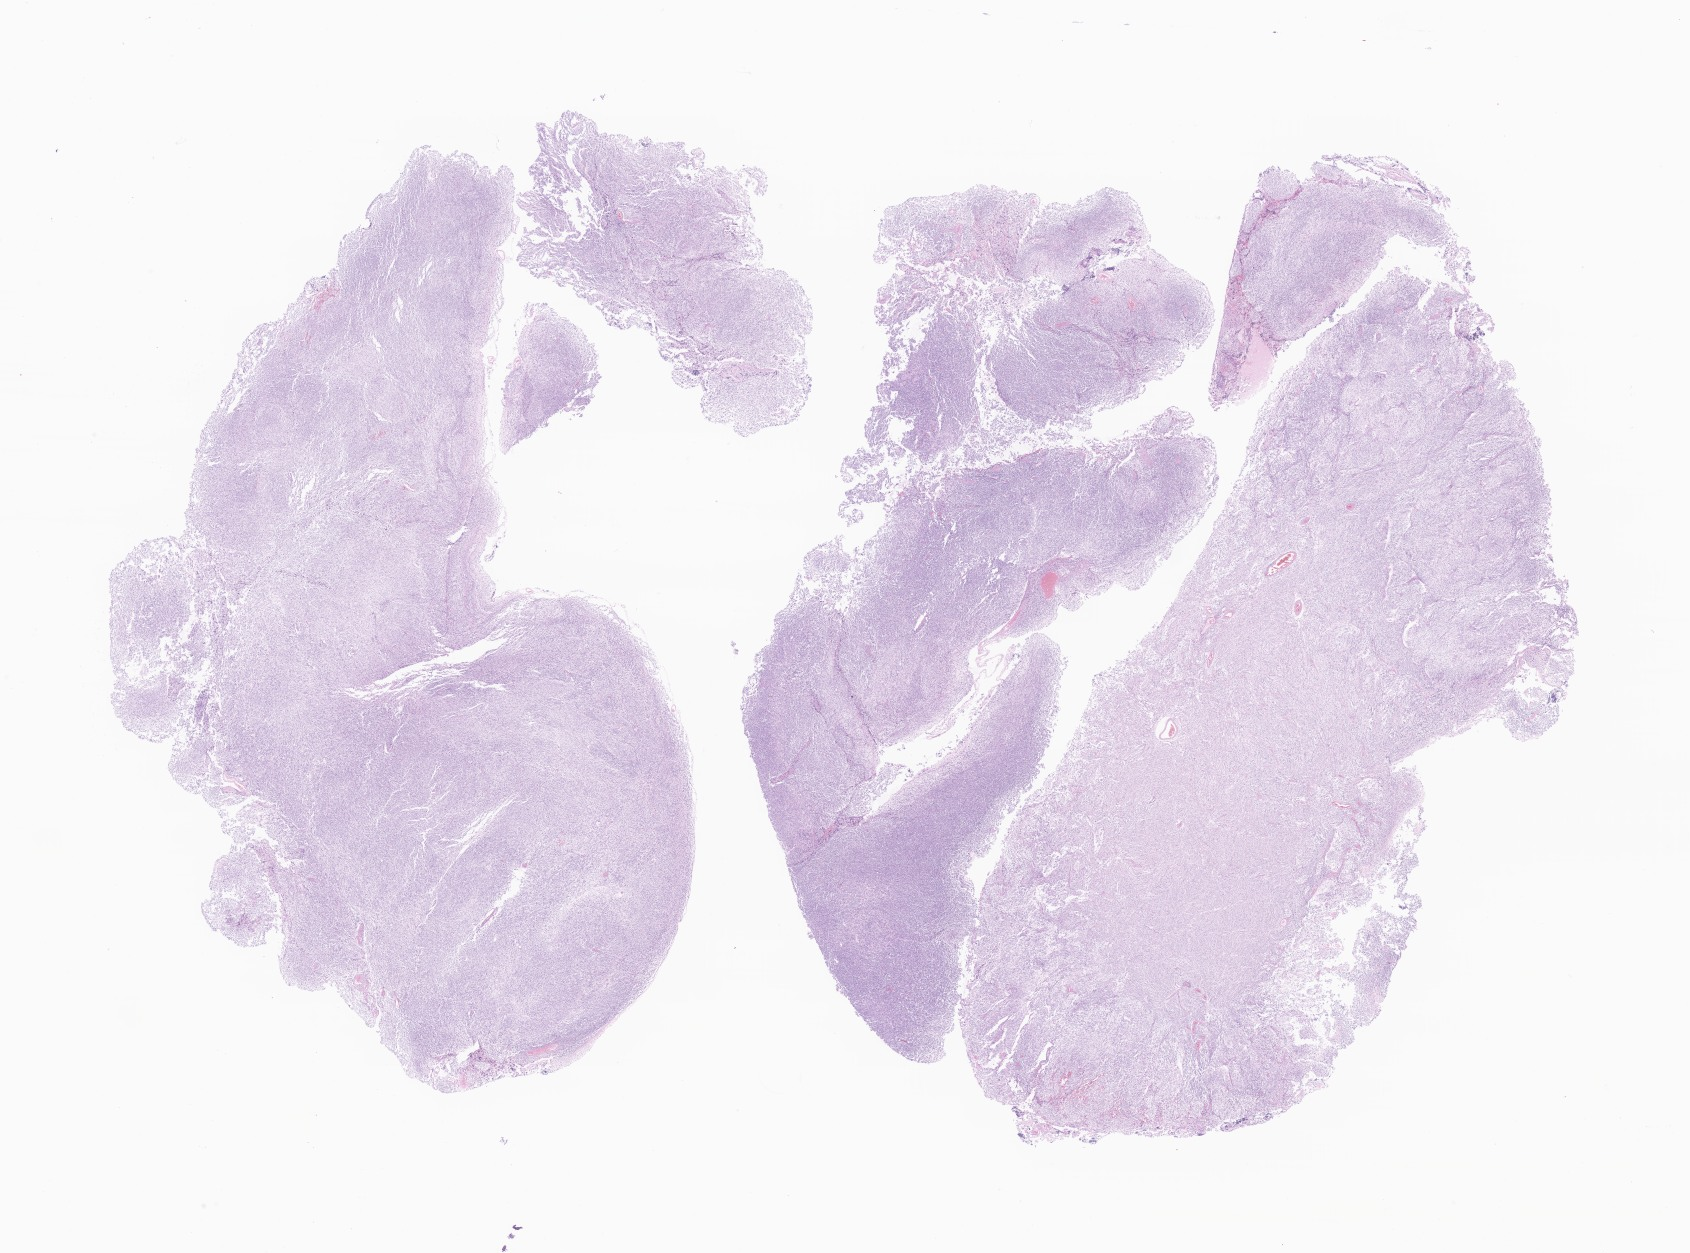
H&E whole-slide image of tumor tissue from the cerebral ventricle — whole scanned area (about 28.5 x 21.1 mm) shown as a low-resolution overview, FFPE section. Patient: male, age 102 months.
- diagnosis: Medulloblastoma, NOS